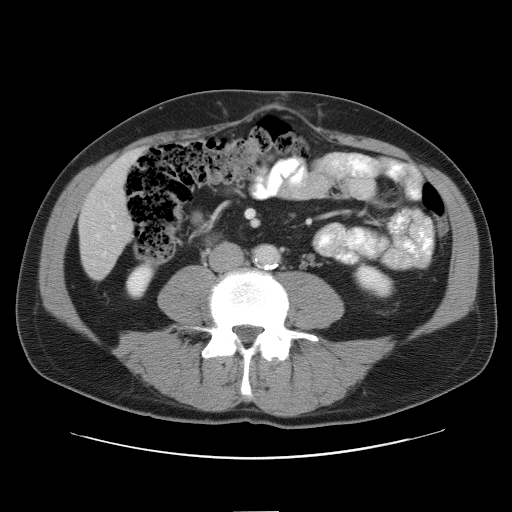
Contrast-enhanced abdominal CT, one axial slice. Position 15 of 52 along the scan axis. Reconstruction kernel STANDARD. Intravenous contrast given. Soft-tissue window (W 400 / L 40 HU). 5 mm slice thickness. 512 × 512 image matrix, field of view 393 × 393 mm. Male patient, age 70 years. From the clinical record (not read from this slice): diagnosis: colorectal cancer liver metastases, imaged before liver resection; multiple liver metastases: yes; largest metastasis: 4 cm.
Structures marked on this image (outlined manually by an expert reader):
- hepatic veins: bounding box <97,235,100,237> (left, top, right, bottom; pixels)
- liver: <79,151,140,278>
- planned liver remnant (the part of the liver to remain after resection): <122,151,140,166>
- portal vein (with intrahepatic branches): <112,226,115,229>